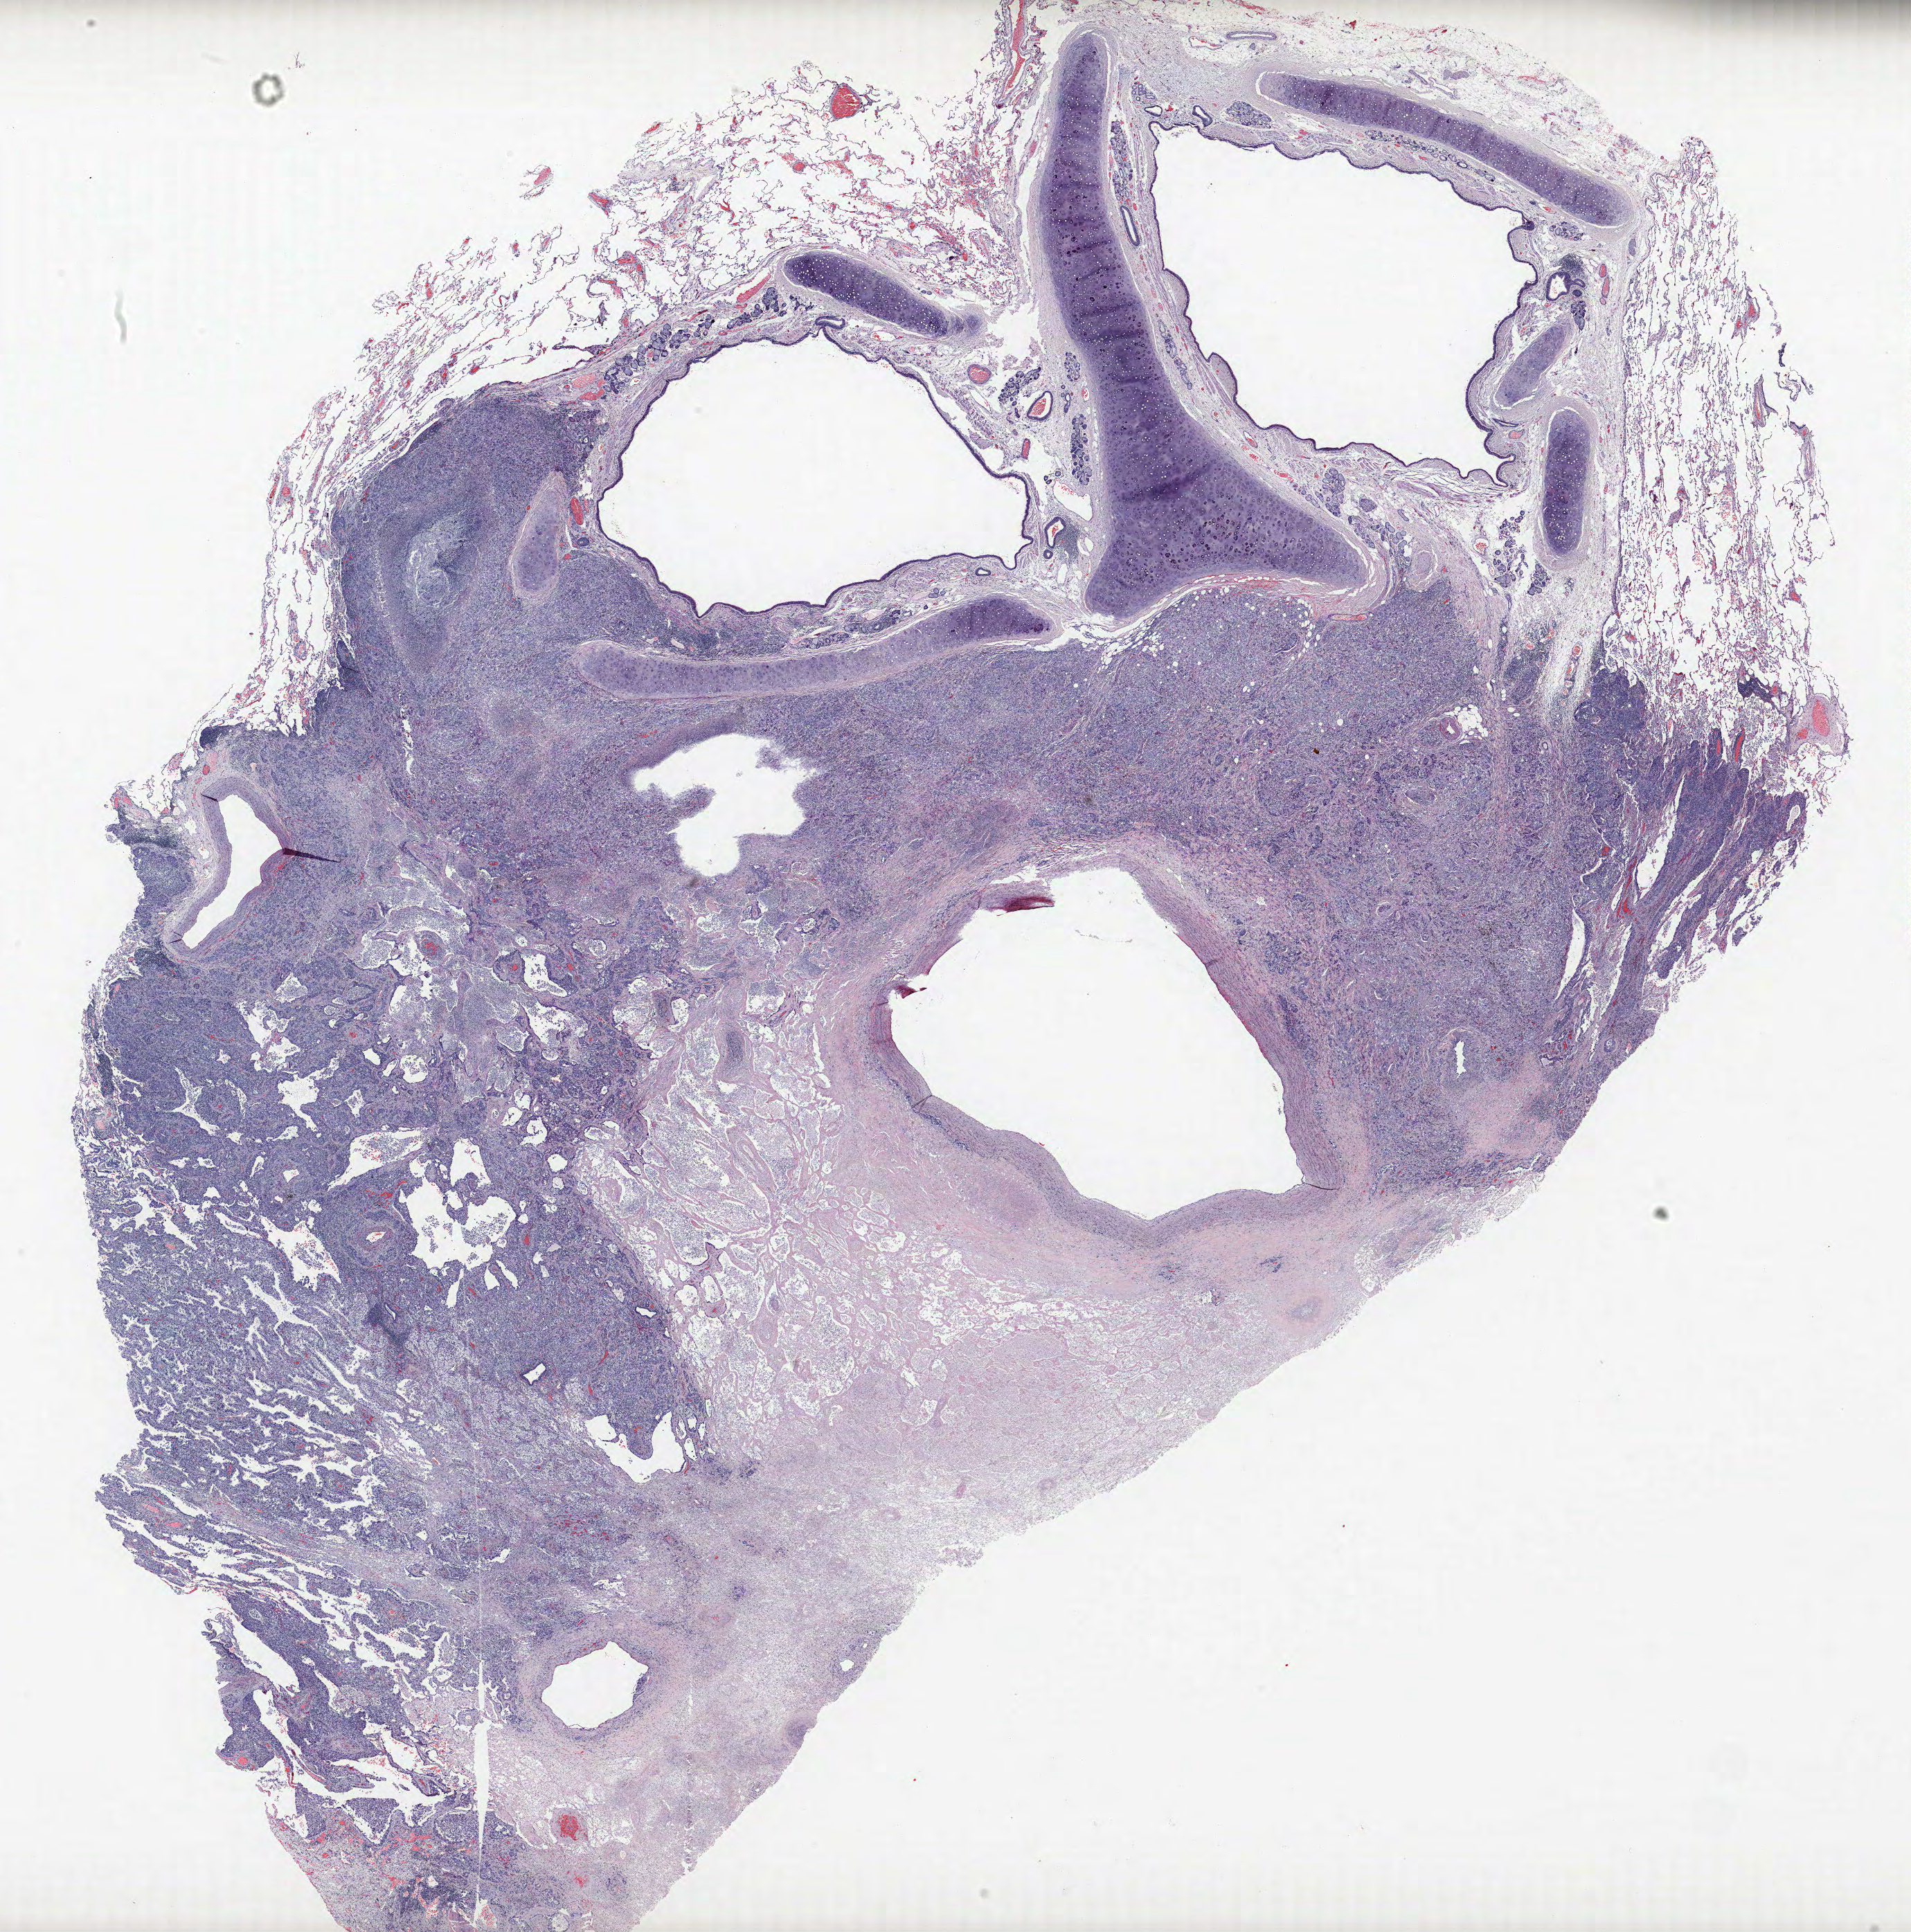
Whole-slide histology image, H&E-stained, whole scanned area (about 22.1 x 22.3 mm, acquisition: 40x scan) shown as a low-resolution overview, FFPE section, lung tissue. Male, age 63 at enrolment. Former smoker at enrolment. Grade: moderately differentiated (G2).
Participant's lung-cancer diagnosis: Adenocarcinoma, NOS (ICD-O-3 8140/3). Tumour size (pathology): 45 mm. Primary tumour location (clinical record): right lower lobe. Stage (AJCC 6th edition): IIIA.